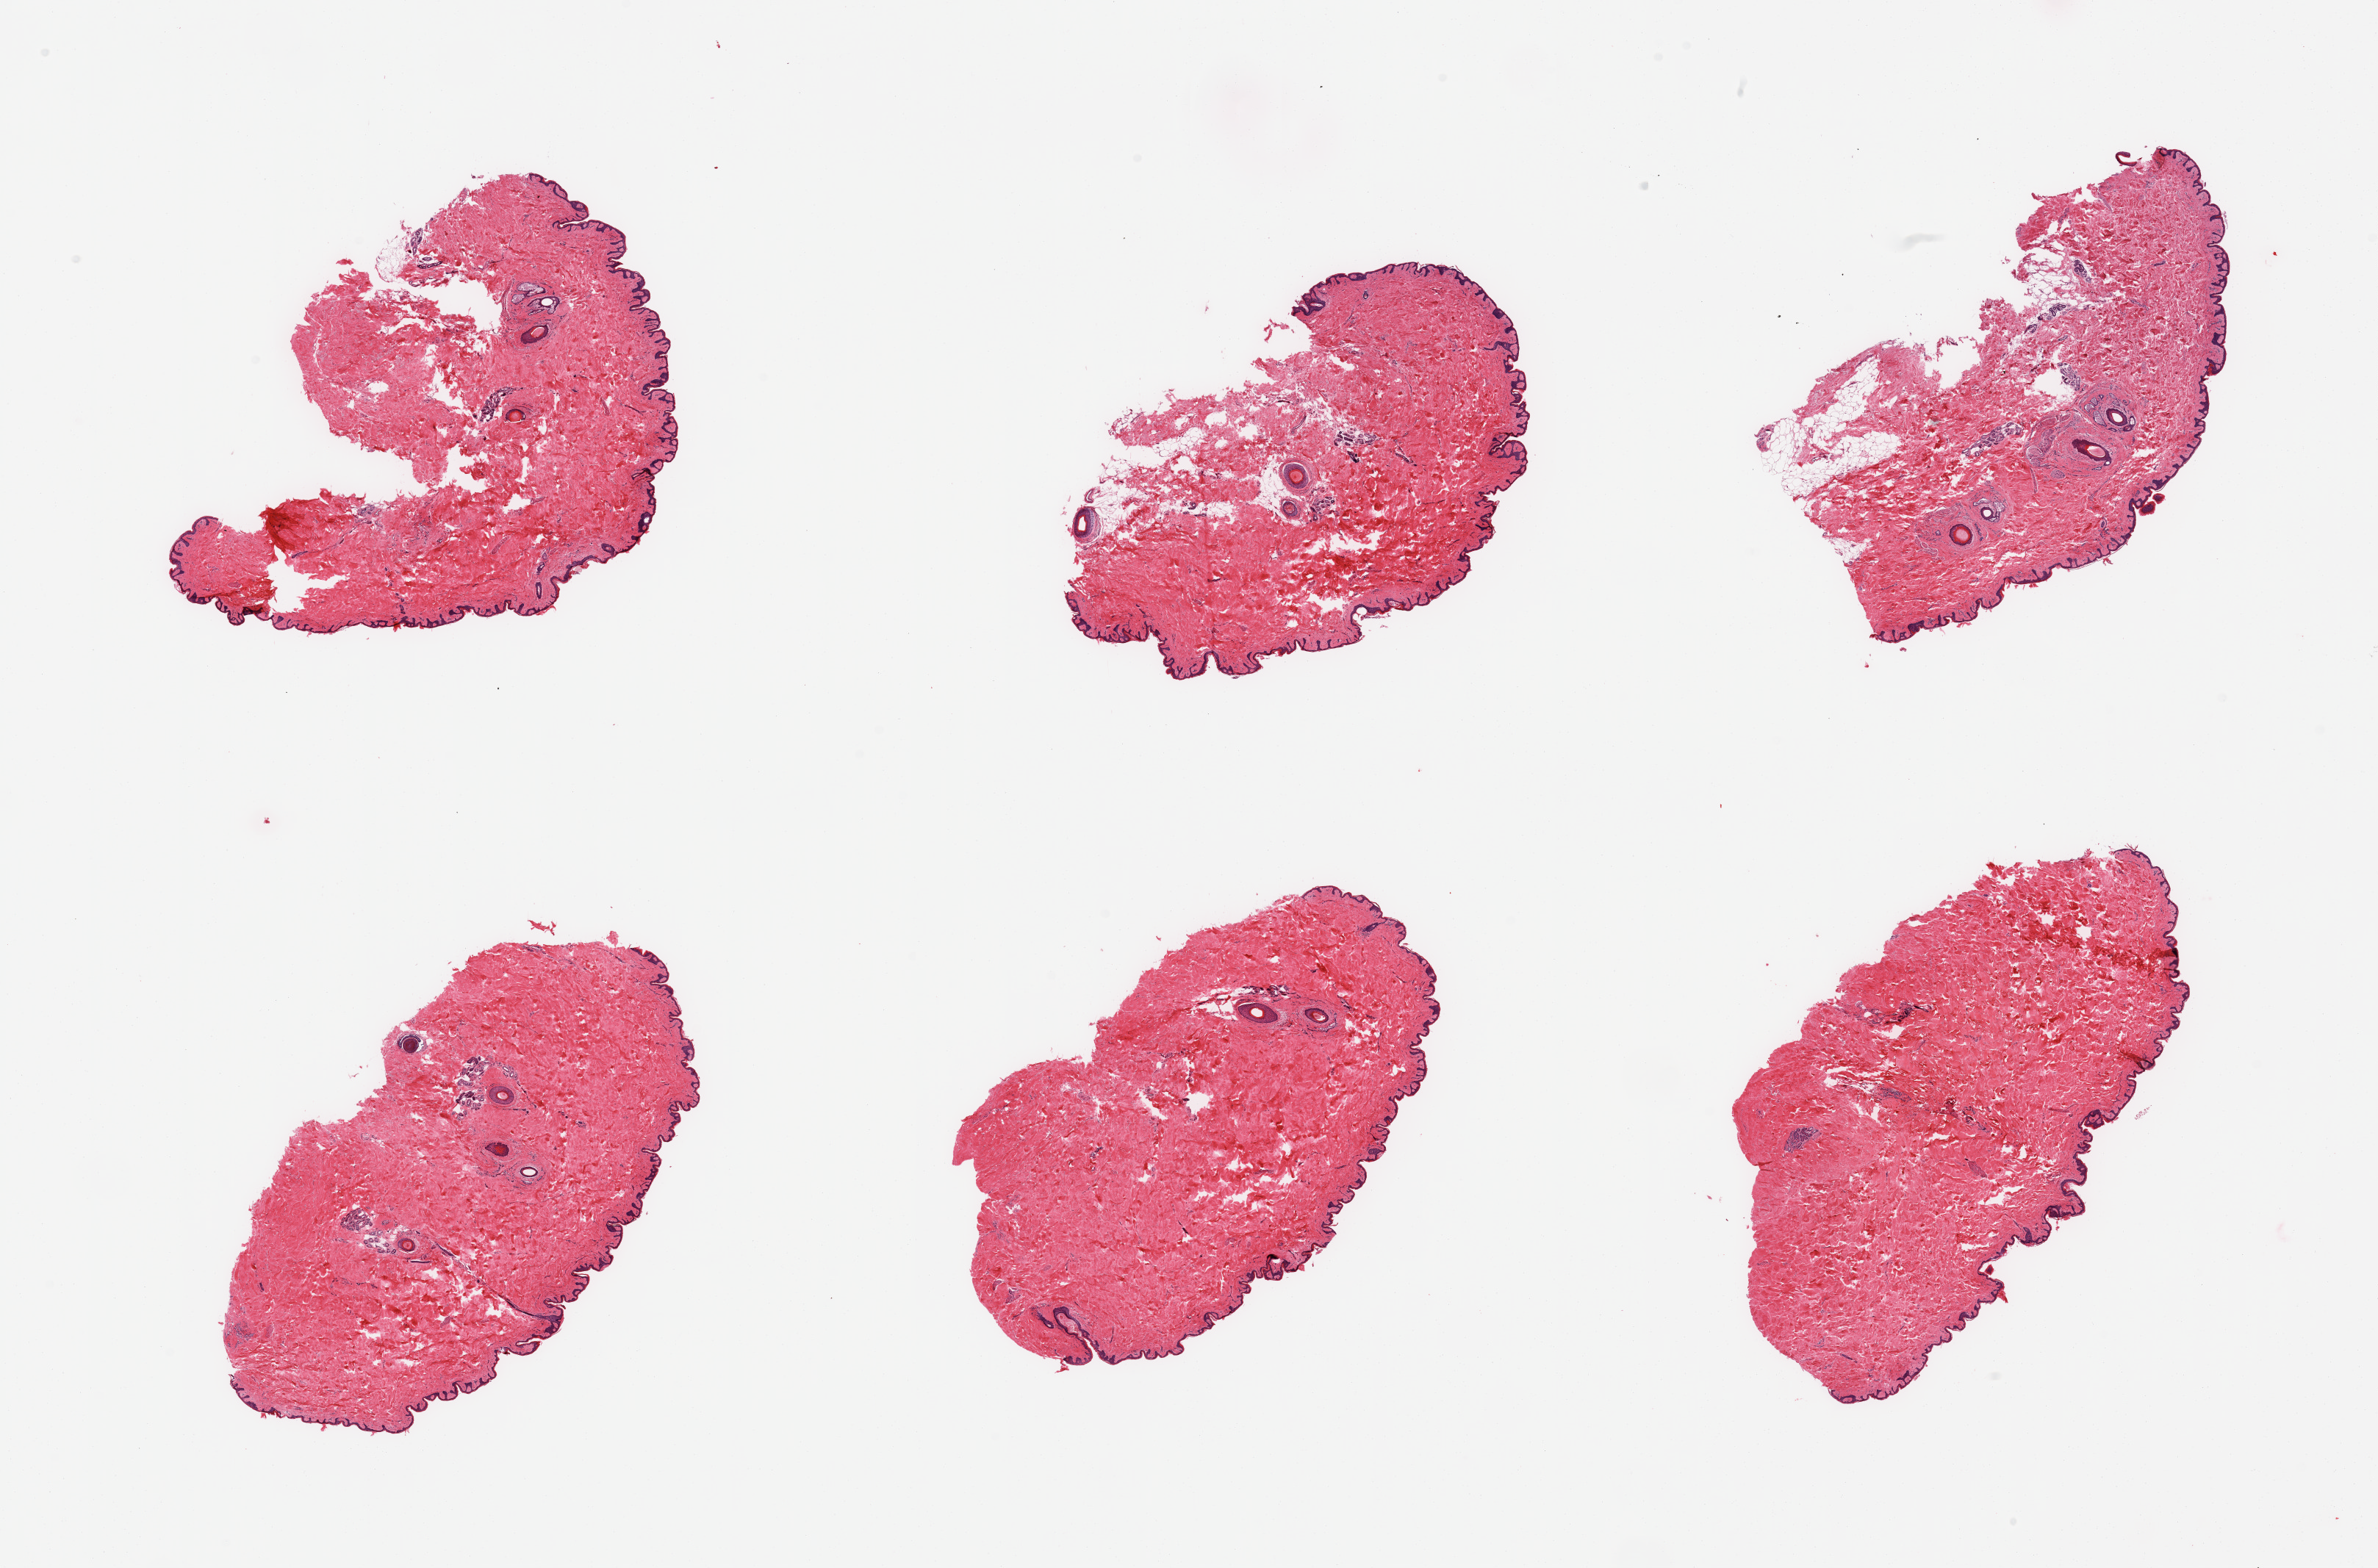
Digitized H&E-stained section, brightfield — whole scanned area (about 25.6 x 16.9 mm, from a 20x scan) shown as a low-resolution overview. PAXgene-fixed, paraffin-embedded tissue. Target tissue: skin of suprapubic region. Tissue donor sample. Donor sex: male.
Reviewer comment on this tissue sample: 6 pieces; well trimmed; 5% dermal fat.